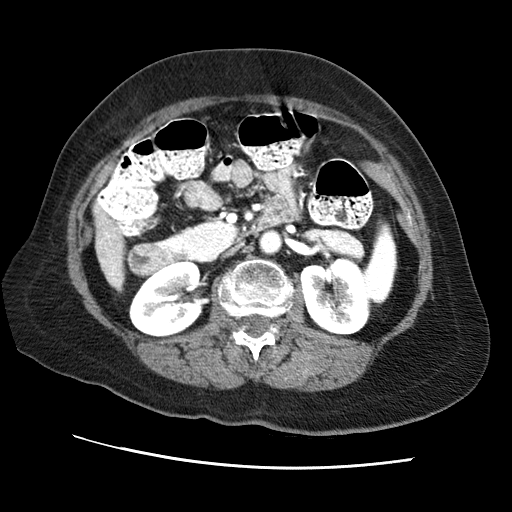
Contrast-enhanced abdominal CT (liver protocol), one axial slice; position 16 of 65 along the scan axis; soft-tissue window (W 400 / L 40 HU); 2.5 mm slice thickness; 512 × 512 image matrix, field of view 340 × 340 mm. From the clinical record (not read from this slice): diagnosis: hepatocellular carcinoma (patient treated with transarterial chemoembolisation; whether this scan precedes or follows treatment is not stated here); TNM stage (as recorded): Stage-II; Child-Pugh class: A; tumour differentiation: no biopsy; tumour size: 2.5 cm.
Outlined on this slice (semi-automatically segmented with operator editing):
- liver parenchyma outside the tumour (the mass and vessels are separate outlines, so this box may not span the whole liver): bounding box <96,214,124,288> (left, top, right, bottom; pixels)
- liver vessels: <102,232,117,281>